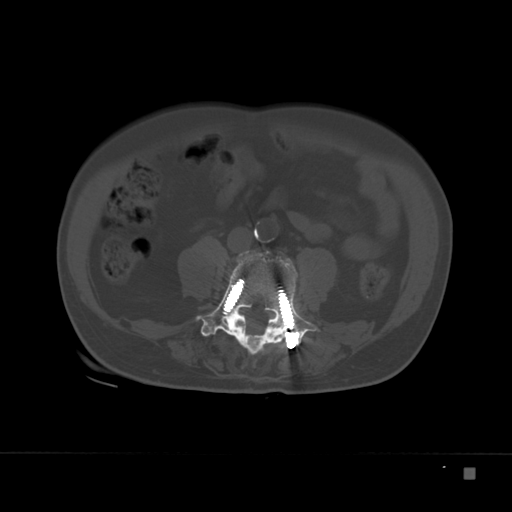
CT including the spine, one axial slice. Position 47 of 332 along the scan axis. Reconstruction kernel Br40s. Bone window (W 1800 / L 400 HU). 512 × 512 image matrix. Male patient, age 72 years. Case-level facts recorded for this patient, not image findings: primary cancer: skeletal.
Annotated regions visible in this slice (semi-automatically segmented with operator editing):
- L4 vertebra: box from (x=196, y=249) to (x=320, y=355) px